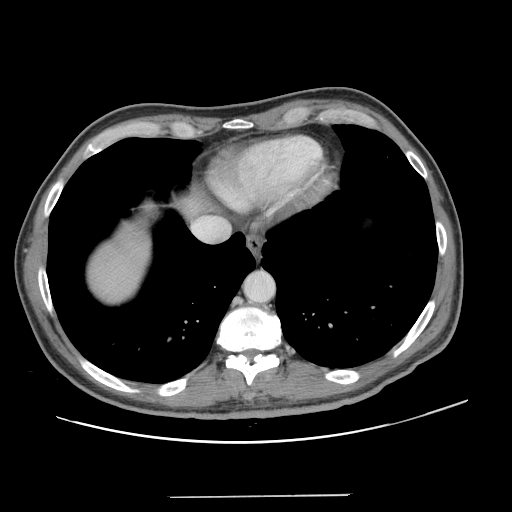
Contrast-enhanced abdominal CT, one axial slice. Slice 120 of 131 in the series (ordered by position). Intravenous contrast given. Soft-tissue window (W 400 / L 40 HU). 2.5 mm slice thickness. 512 × 512 image matrix, field of view 403 × 403 mm. Male patient, age 60 years. Case-level facts recorded for this patient, not image findings: diagnosis: colorectal cancer liver metastases, imaged before liver resection; multiple liver metastases: no; largest metastasis: 2.5 cm; disease in both lobes: no.
Annotated regions visible in this slice (manually delineated by an expert):
- liver: bounding box (x1, y1, x2, y2) in pixels: (89, 234, 149, 302)
- planned liver remnant (the part of the liver to remain after resection): (89, 235, 149, 303)